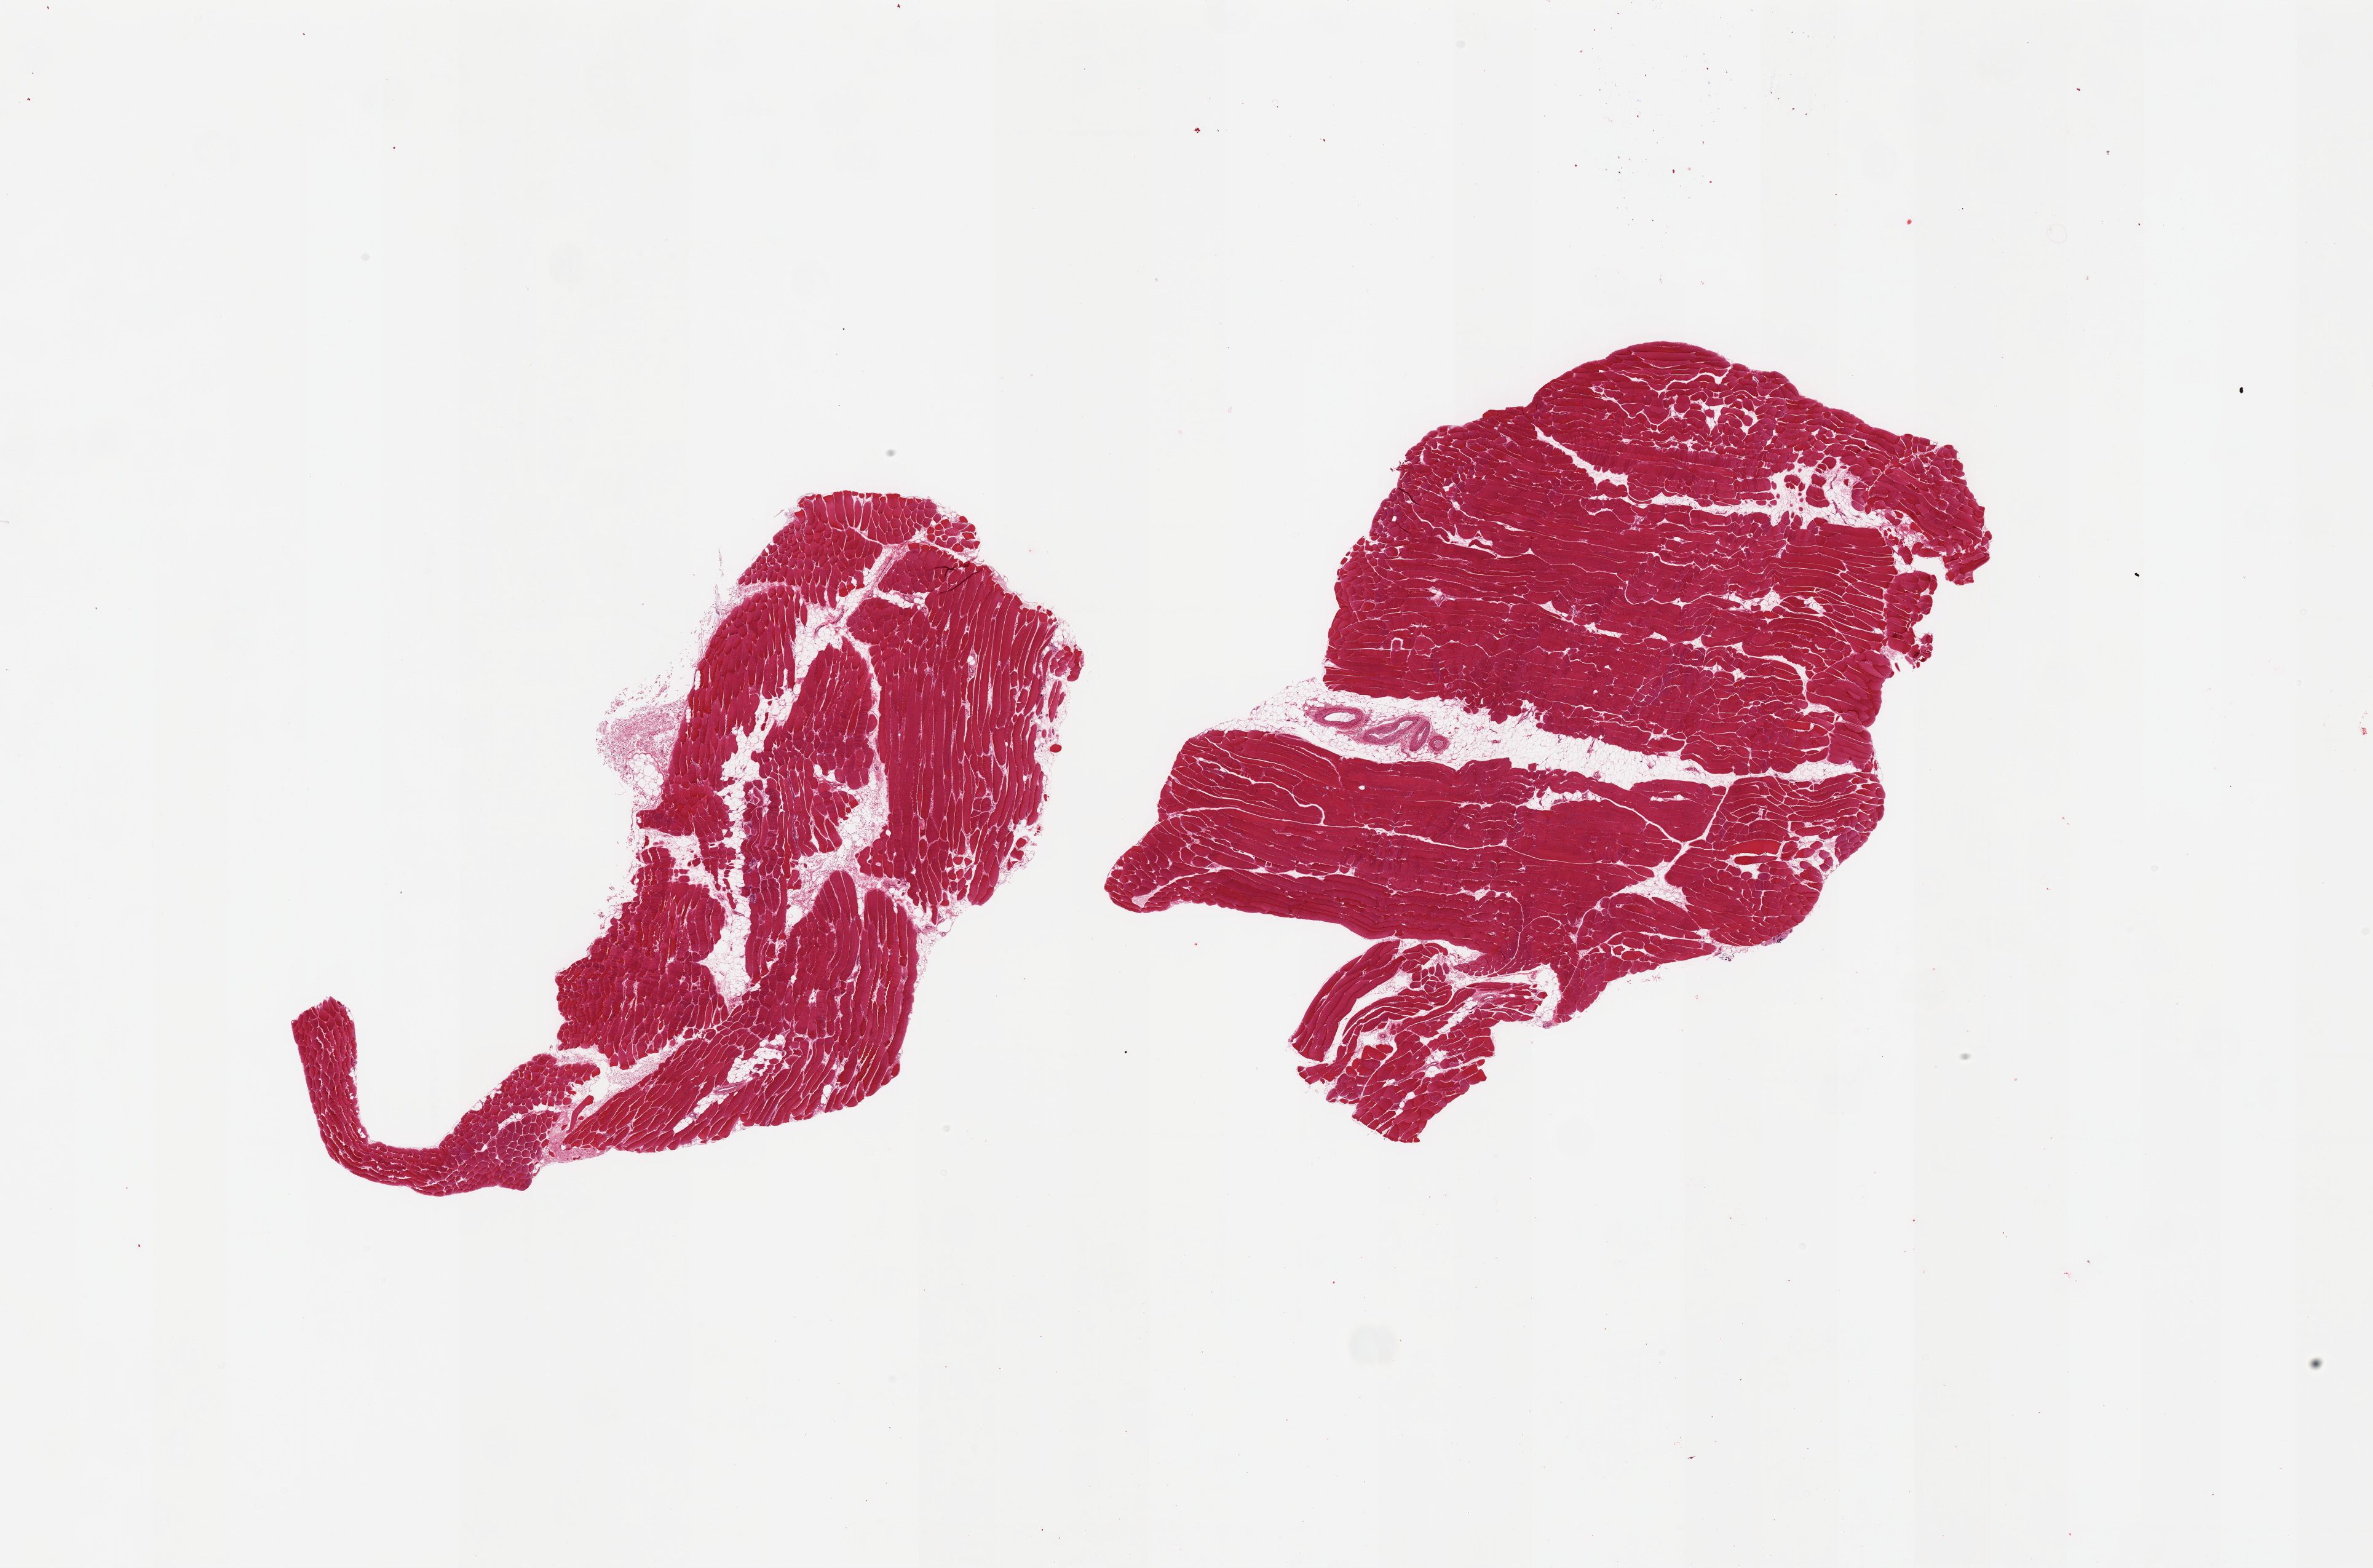
Whole-slide image, haematoxylin and eosin stain, brightfield, shown as a low-resolution overview of the whole scanned area (about 30.5 x 20.2 mm); PAXgene-fixed, paraffin-embedded tissue; sampled site (target tissue): skeletal muscle; tissue donor sample. Male donor.
Review note (as recorded): 2 pieces; 10% internal fat.